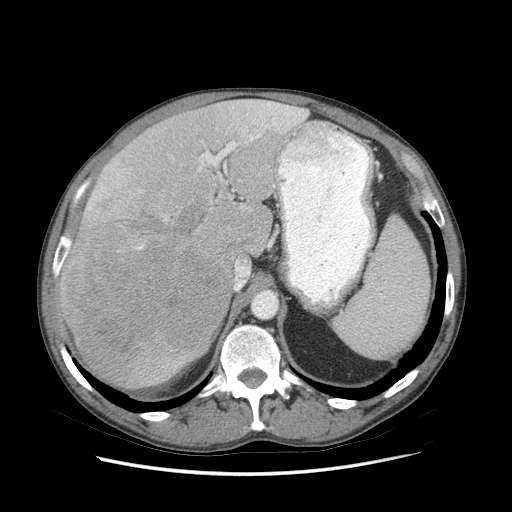
Contrast-enhanced abdominal CT (liver protocol), one axial slice. Slice 53 of 89 in the series (ordered by position). Reconstruction kernel STANDARD. 140 kVp. Soft-tissue window (W 400 / L 40 HU). 2.5 mm slice thickness. 512 × 512 image matrix, field of view 380 × 380 mm. Case-level facts recorded for this patient, not image findings: diagnosis: hepatocellular carcinoma (patient treated with transarterial chemoembolisation; whether this scan precedes or follows treatment is not stated here); TNM stage (as recorded): Stage-IIIB; Child-Pugh class: A; tumour differentiation: moderately differentiated; tumour nodularity: multinodular.
Annotated regions visible in this slice (semi-automatic segmentation, software-assisted and operator-edited):
- liver parenchyma outside the tumour (the mass and vessels are separate outlines, so this box may not span the whole liver): box from (x=58, y=100) to (x=306, y=388) px
- mass: (x=59, y=211)–(x=233, y=388)
- liver vessels: (x=62, y=101)–(x=305, y=262)